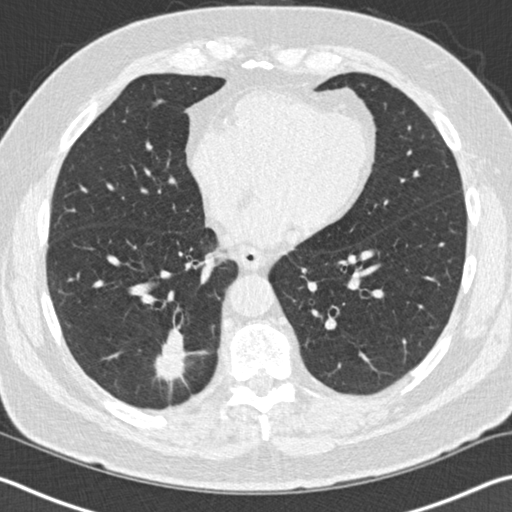
Low-dose screening chest CT, one axial slice. Position 42 of 141 along the scan axis. Reconstruction kernel B30f. 120 kVp. Lung window (W 1500 / L -600 HU). 2 mm slice thickness. 512 × 512 image matrix, field of view 344 × 344 mm.
Outlined on this slice (outlined manually by an expert reader):
- lesion 1 (tumor, lower lobe of right lung): bounding box [x1, y1, x2, y2] px = [154, 327, 187, 382]